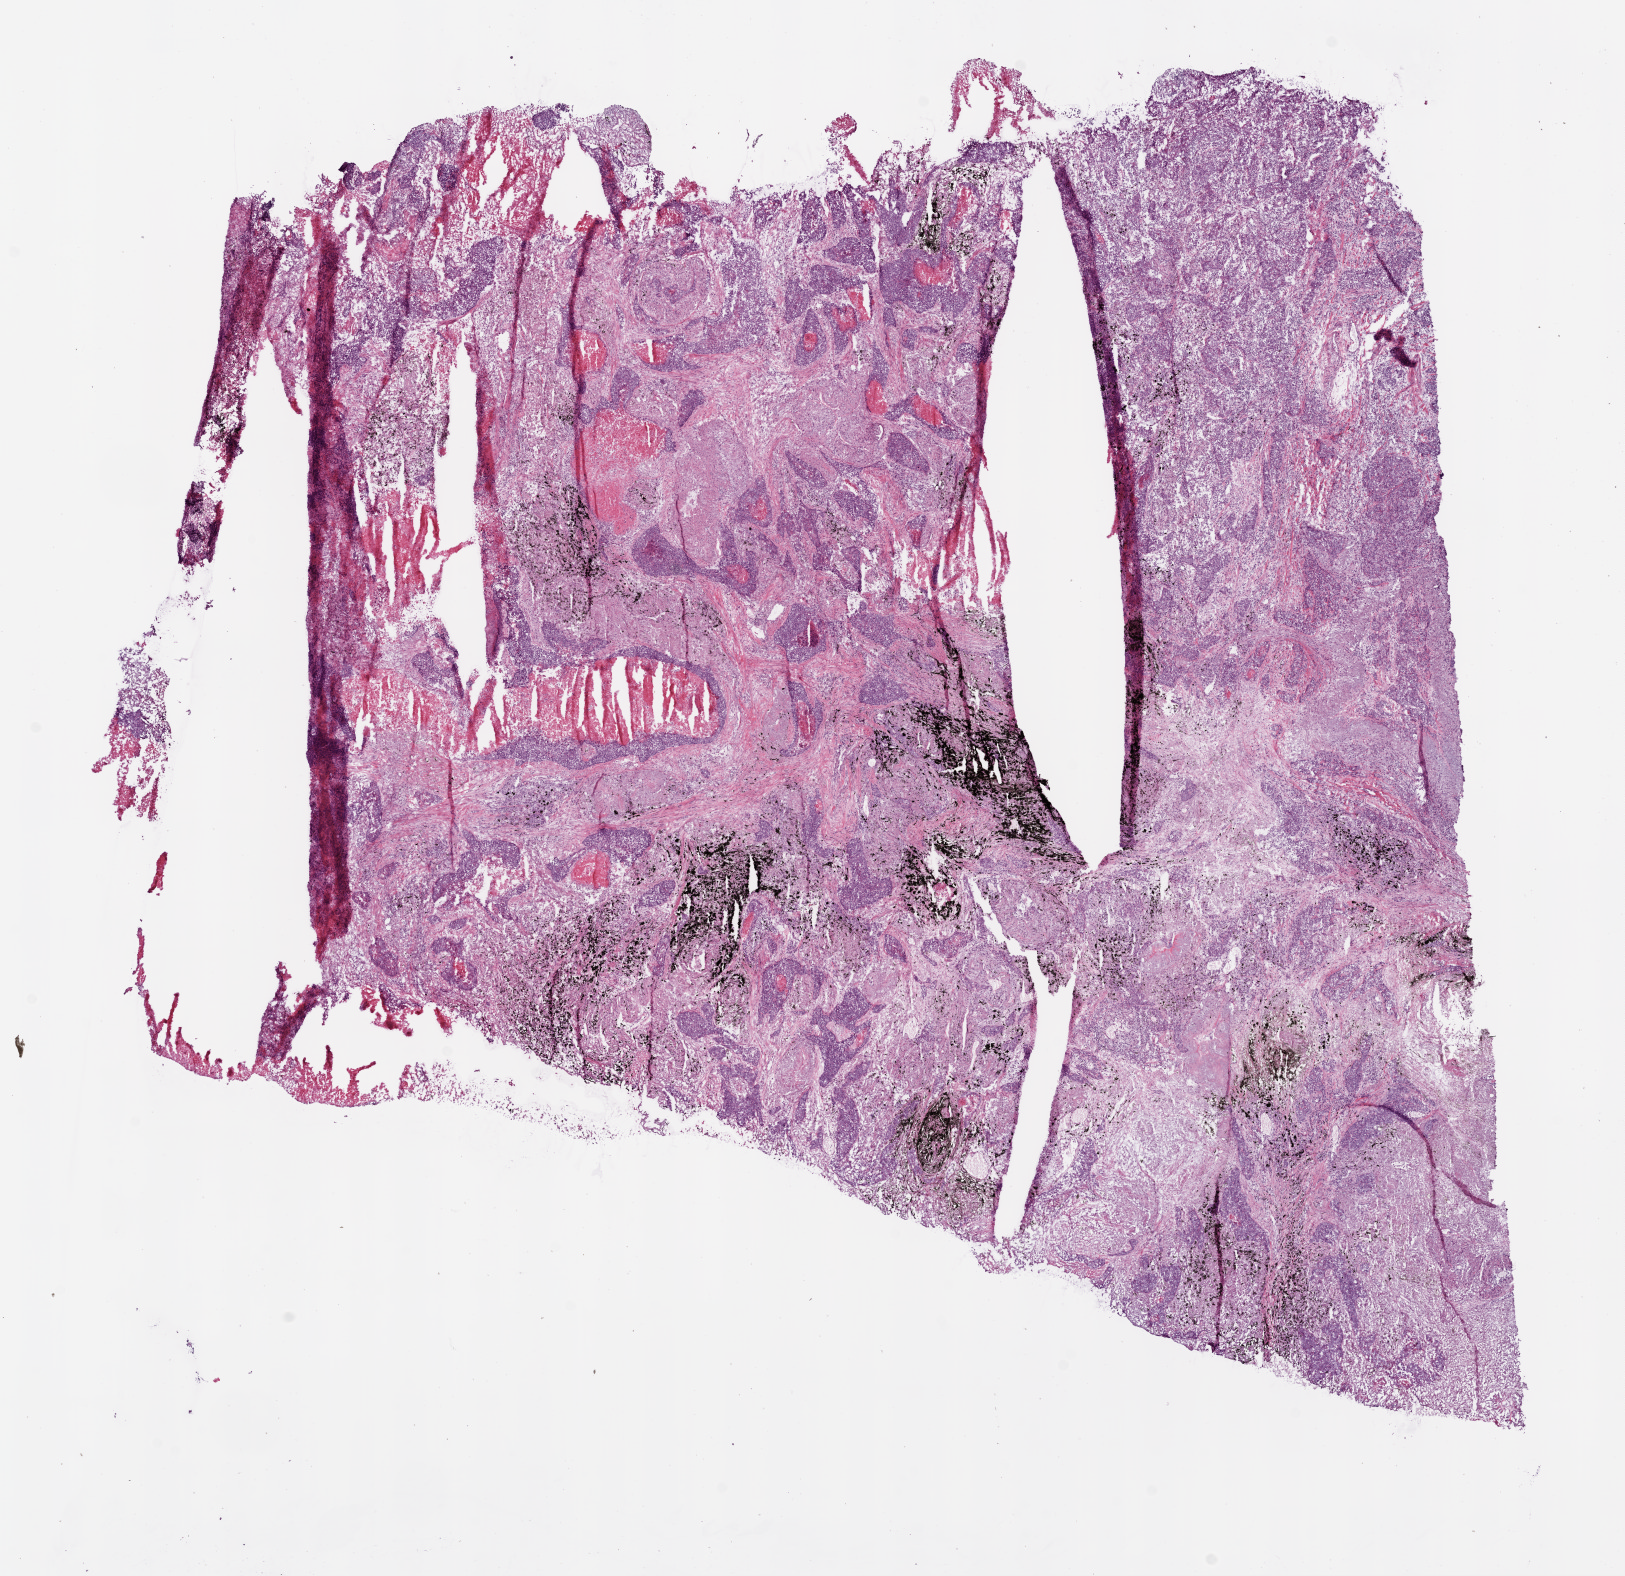
Whole-slide histology image, H&E — whole scanned area (about 13.0 x 12.6 mm) shown as a low-resolution overview; frozen section; primary tumour sample from the lung. Patient: male, age at initial diagnosis 75 years. Slide review estimates, as recorded: tumour cells 55%, tumour nuclei 75%, normal cells 0%, stromal cells 30%, necrosis 15%.
Diagnosis: Squamous cell carcinoma, NOS. AJCC pathologic stage: IIIA.